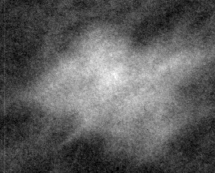
Crop from a digitized film mammogram around one marked abnormality; right breast; MLO view; BI-RADS breast density category 2 (scale 1–4).
Finding: mass, shape irregular, margins microlobulated / spiculated; BI-RADS assessment category 4; pathology (as recorded): malignant.